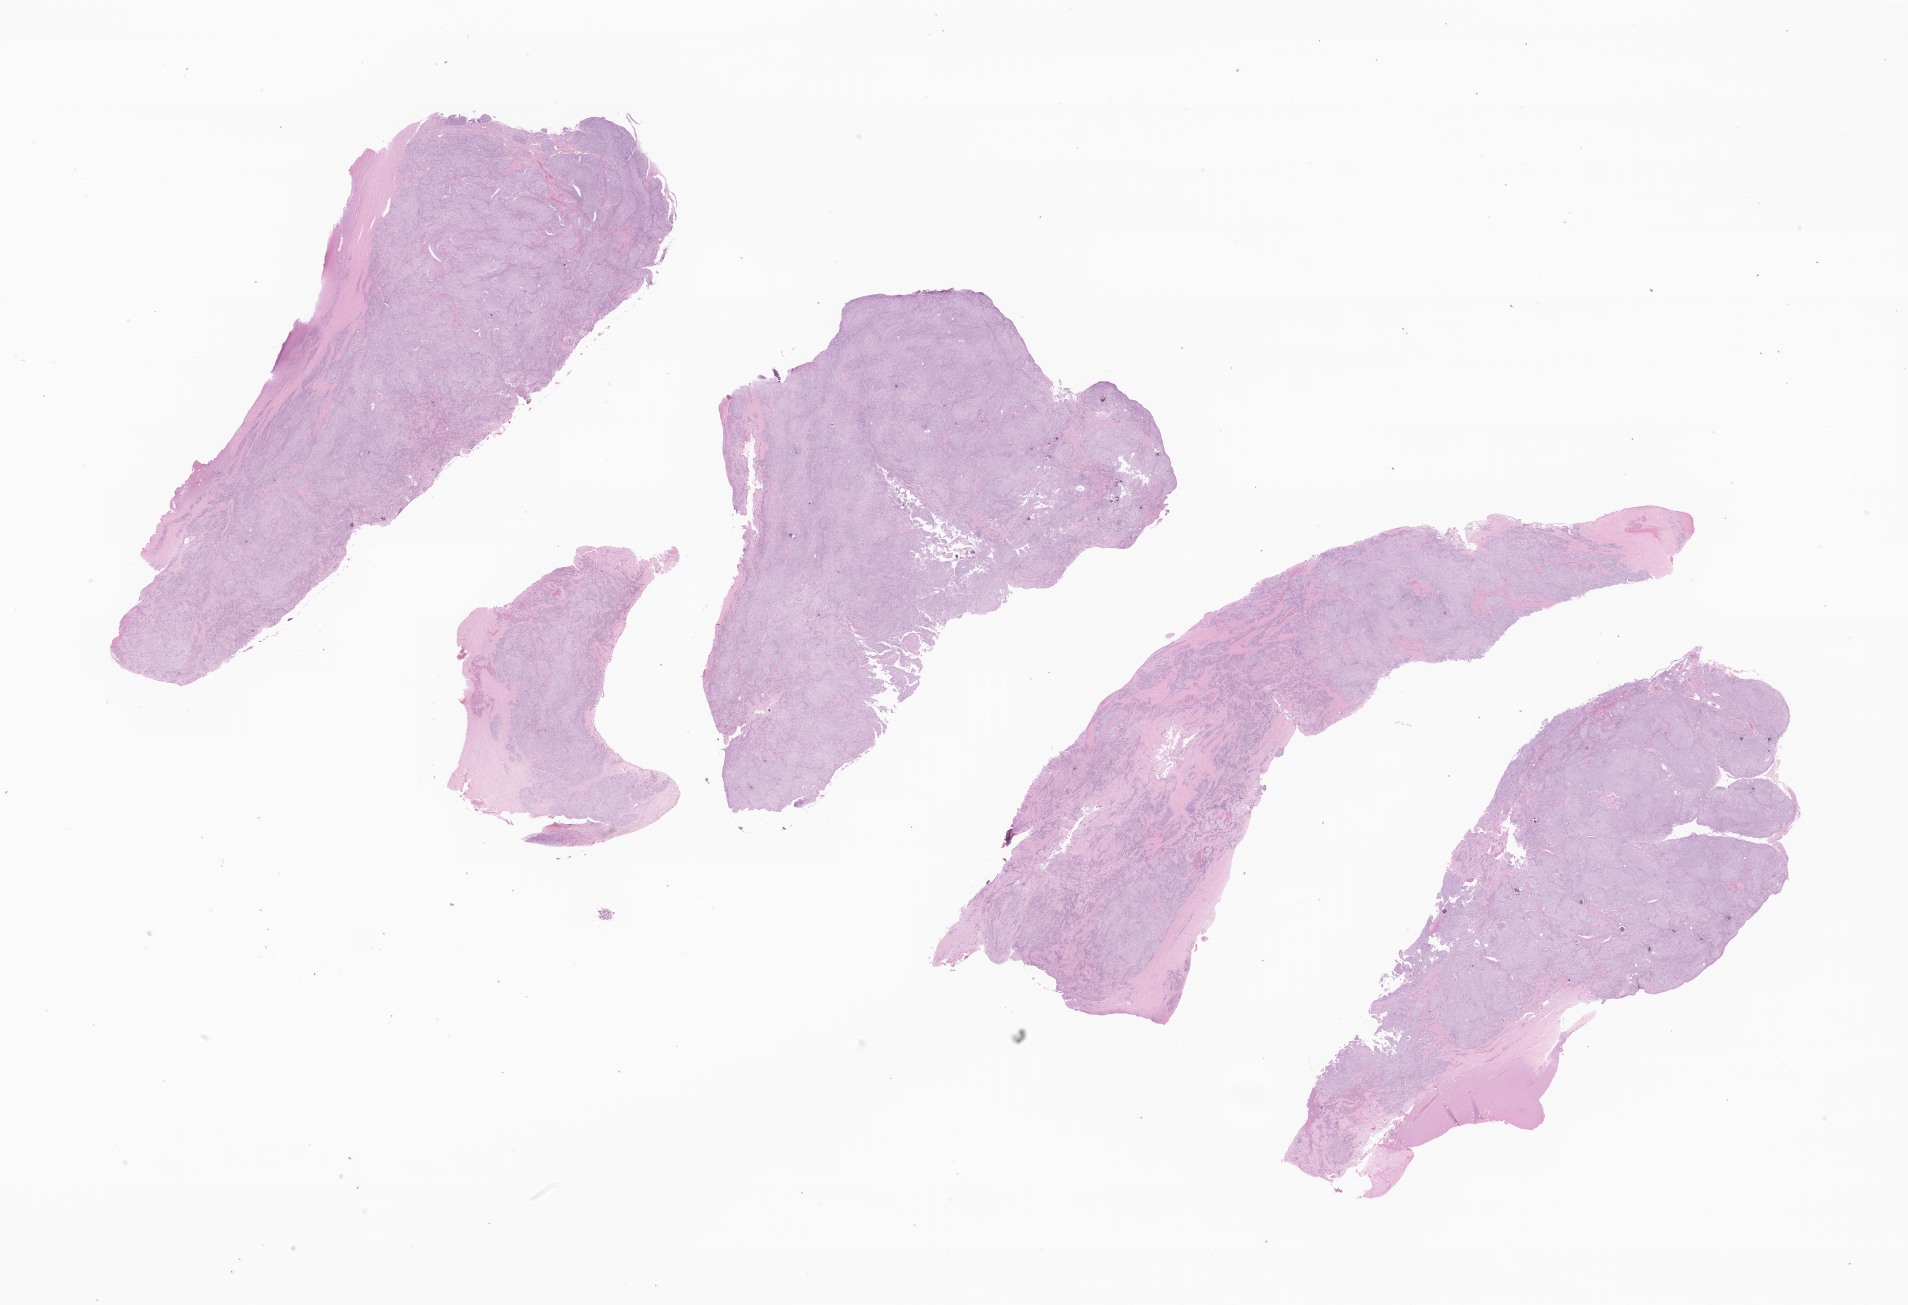
Hematoxylin and eosin (H&E) whole-slide image of tumor tissue from the spinal meninges, whole scanned area (about 32.2 x 22.0 mm) shown as a low-resolution overview. Formalin-fixed paraffin-embedded section. Female patient, age 235 months (19 years 7 months).
Recorded diagnosis: Meningioma, NOS.